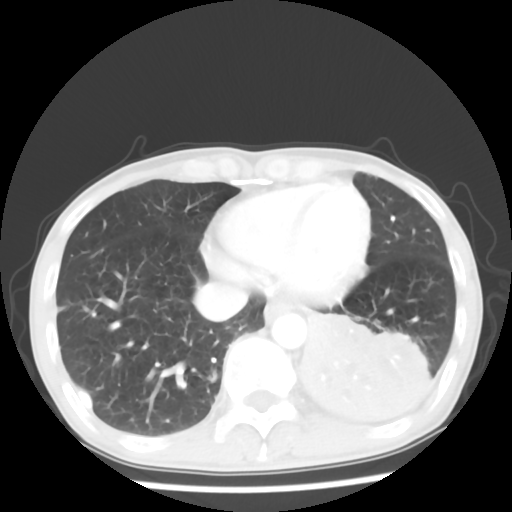
Chest CT, one axial slice; slice 17 of 64 in the series (ordered by position); reconstruction kernel STANDARD; 120 kVp; lung window (W 1500 / L -600 HU); 5 mm slice thickness; 512 × 512 image matrix. Patient: male, 68 years. From the clinical record (not read from this slice): clinical TNM (as recorded): T4 N0 M0.
Structures marked on this image (bounding box drawn by a radiologist):
- lung tumour (recorded histology: squamous cell carcinoma): box from (x=298, y=303) to (x=457, y=441) px